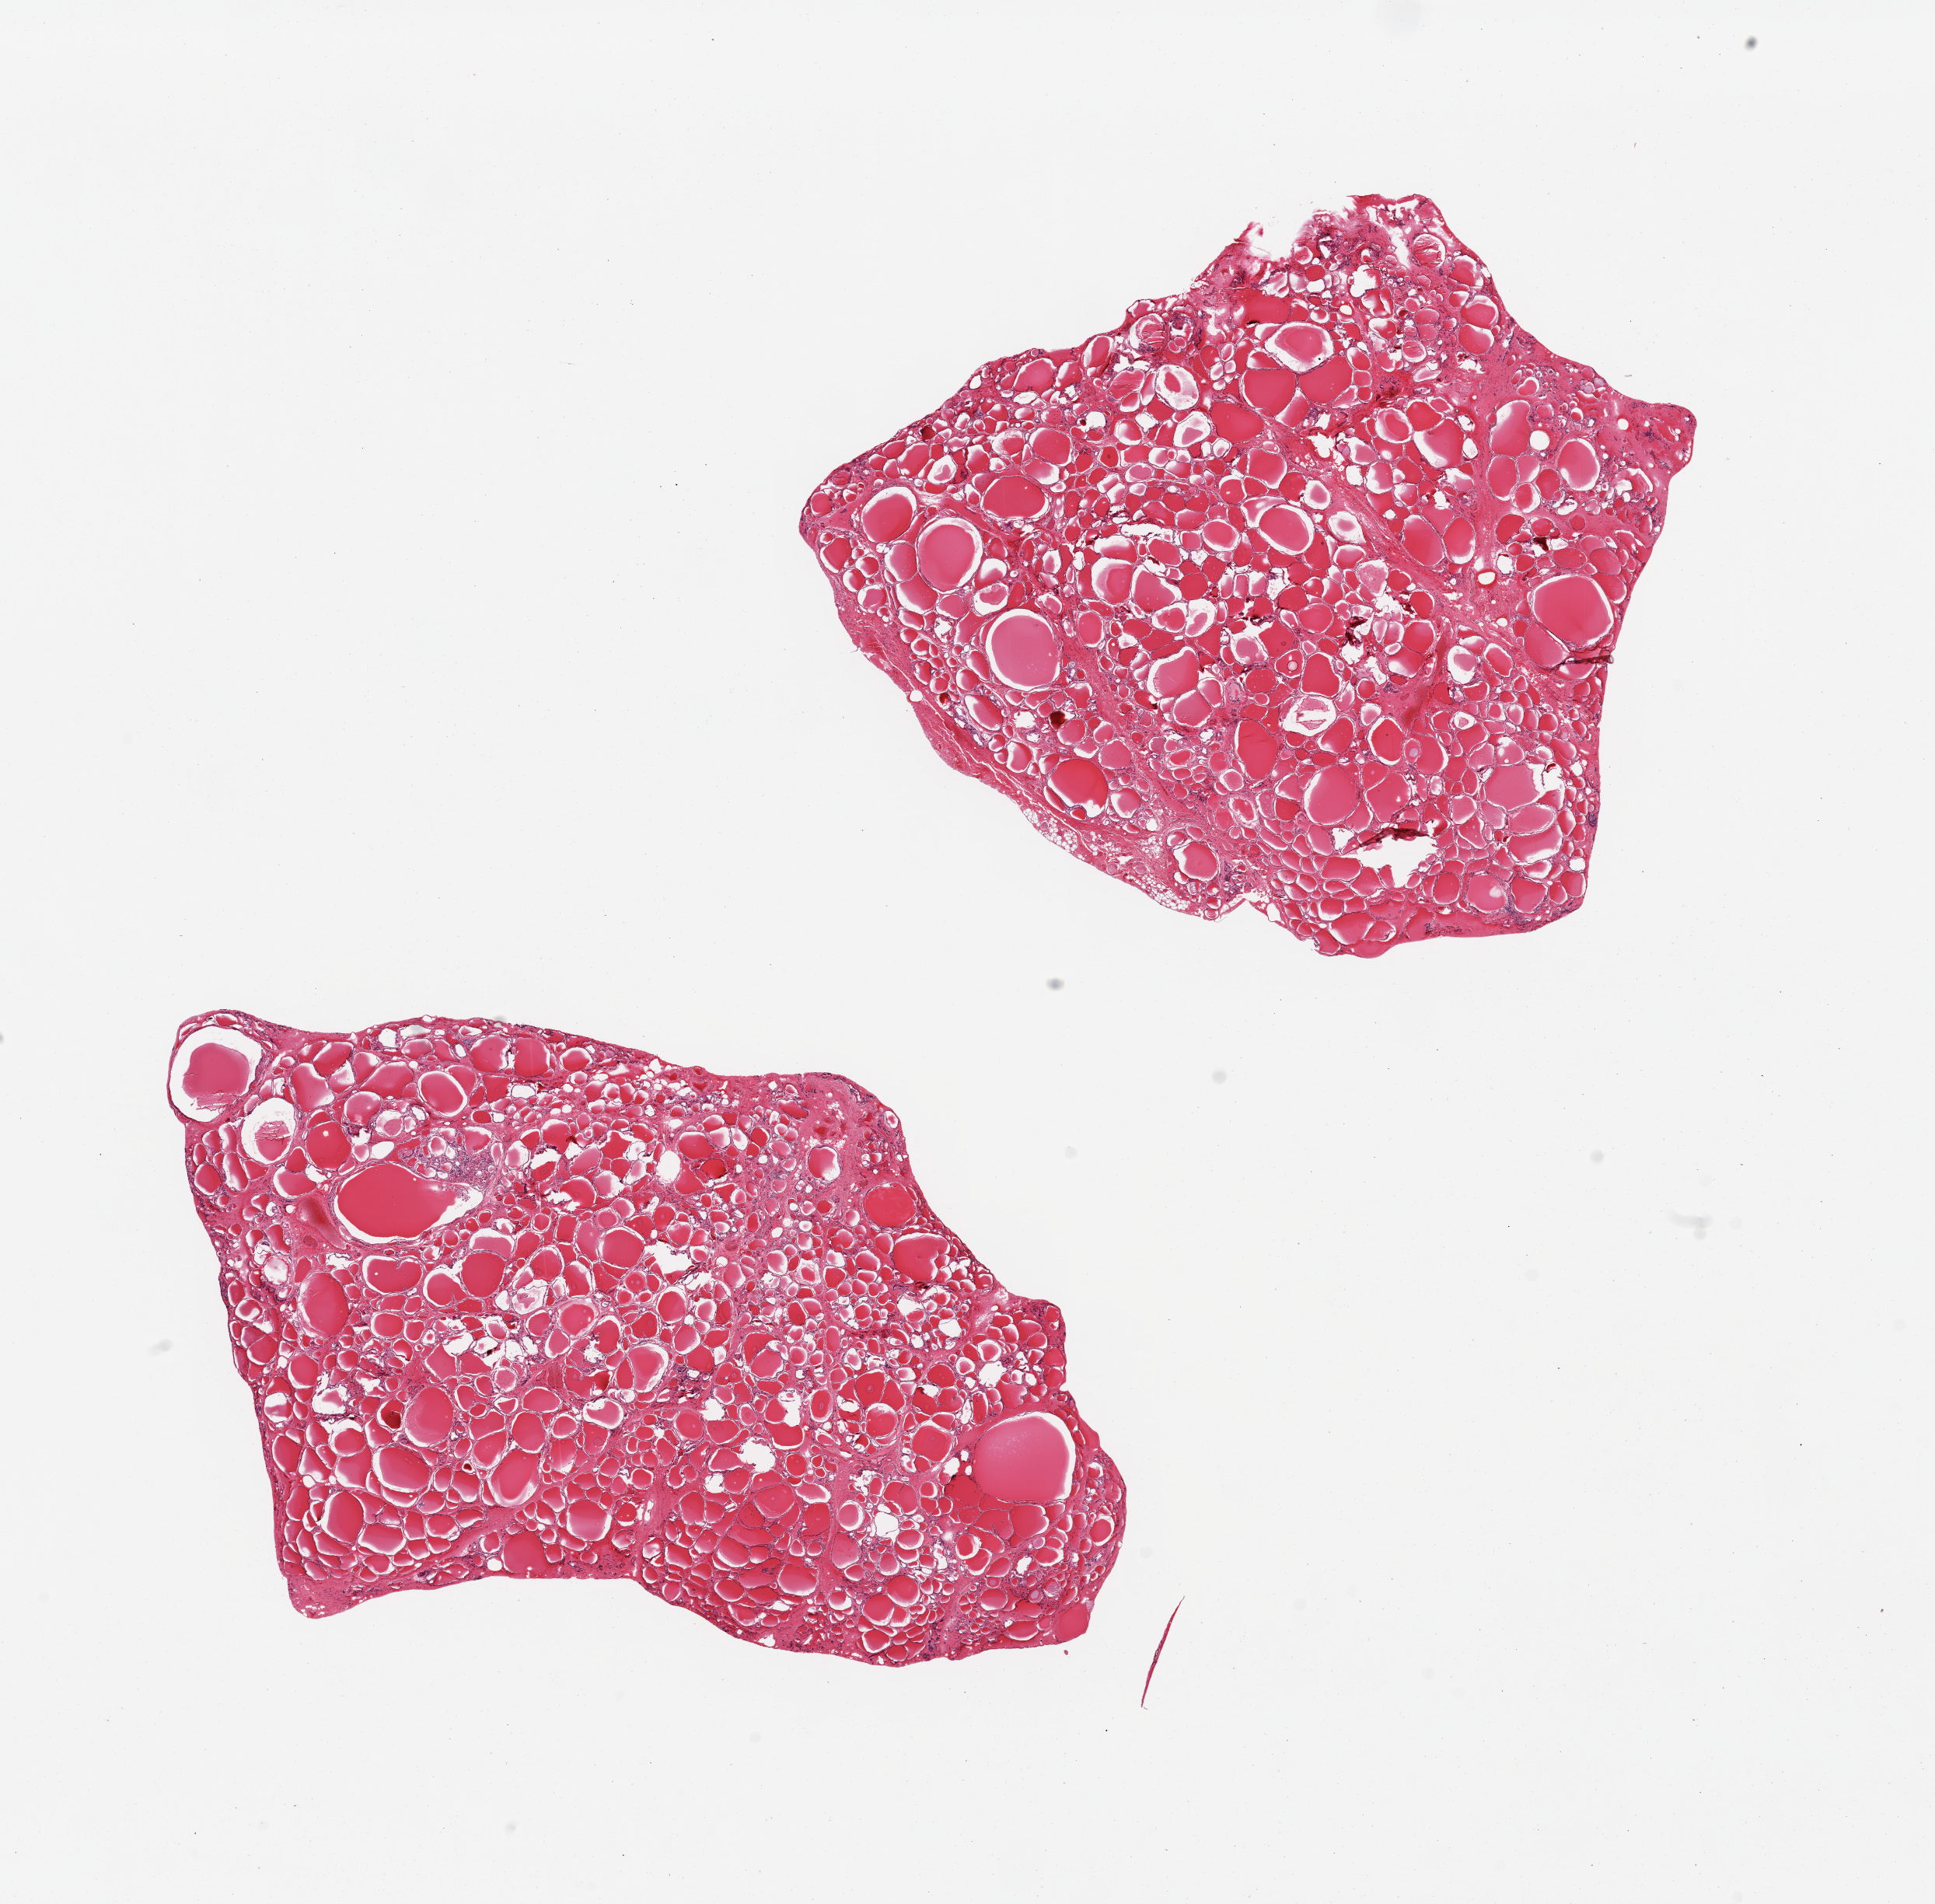
Haematoxylin and eosin whole-slide image, whole scanned area (about 19.7 x 19.4 mm, acquisition: 20x scan) shown as a low-resolution overview. PAXgene-fixed paraffin-embedded (PFPE) section. Target tissue: thyroid. Tissue donor sample. Donor sex: male.
Pathologist's review note for this sample: 2 pieces, no abnormalities.